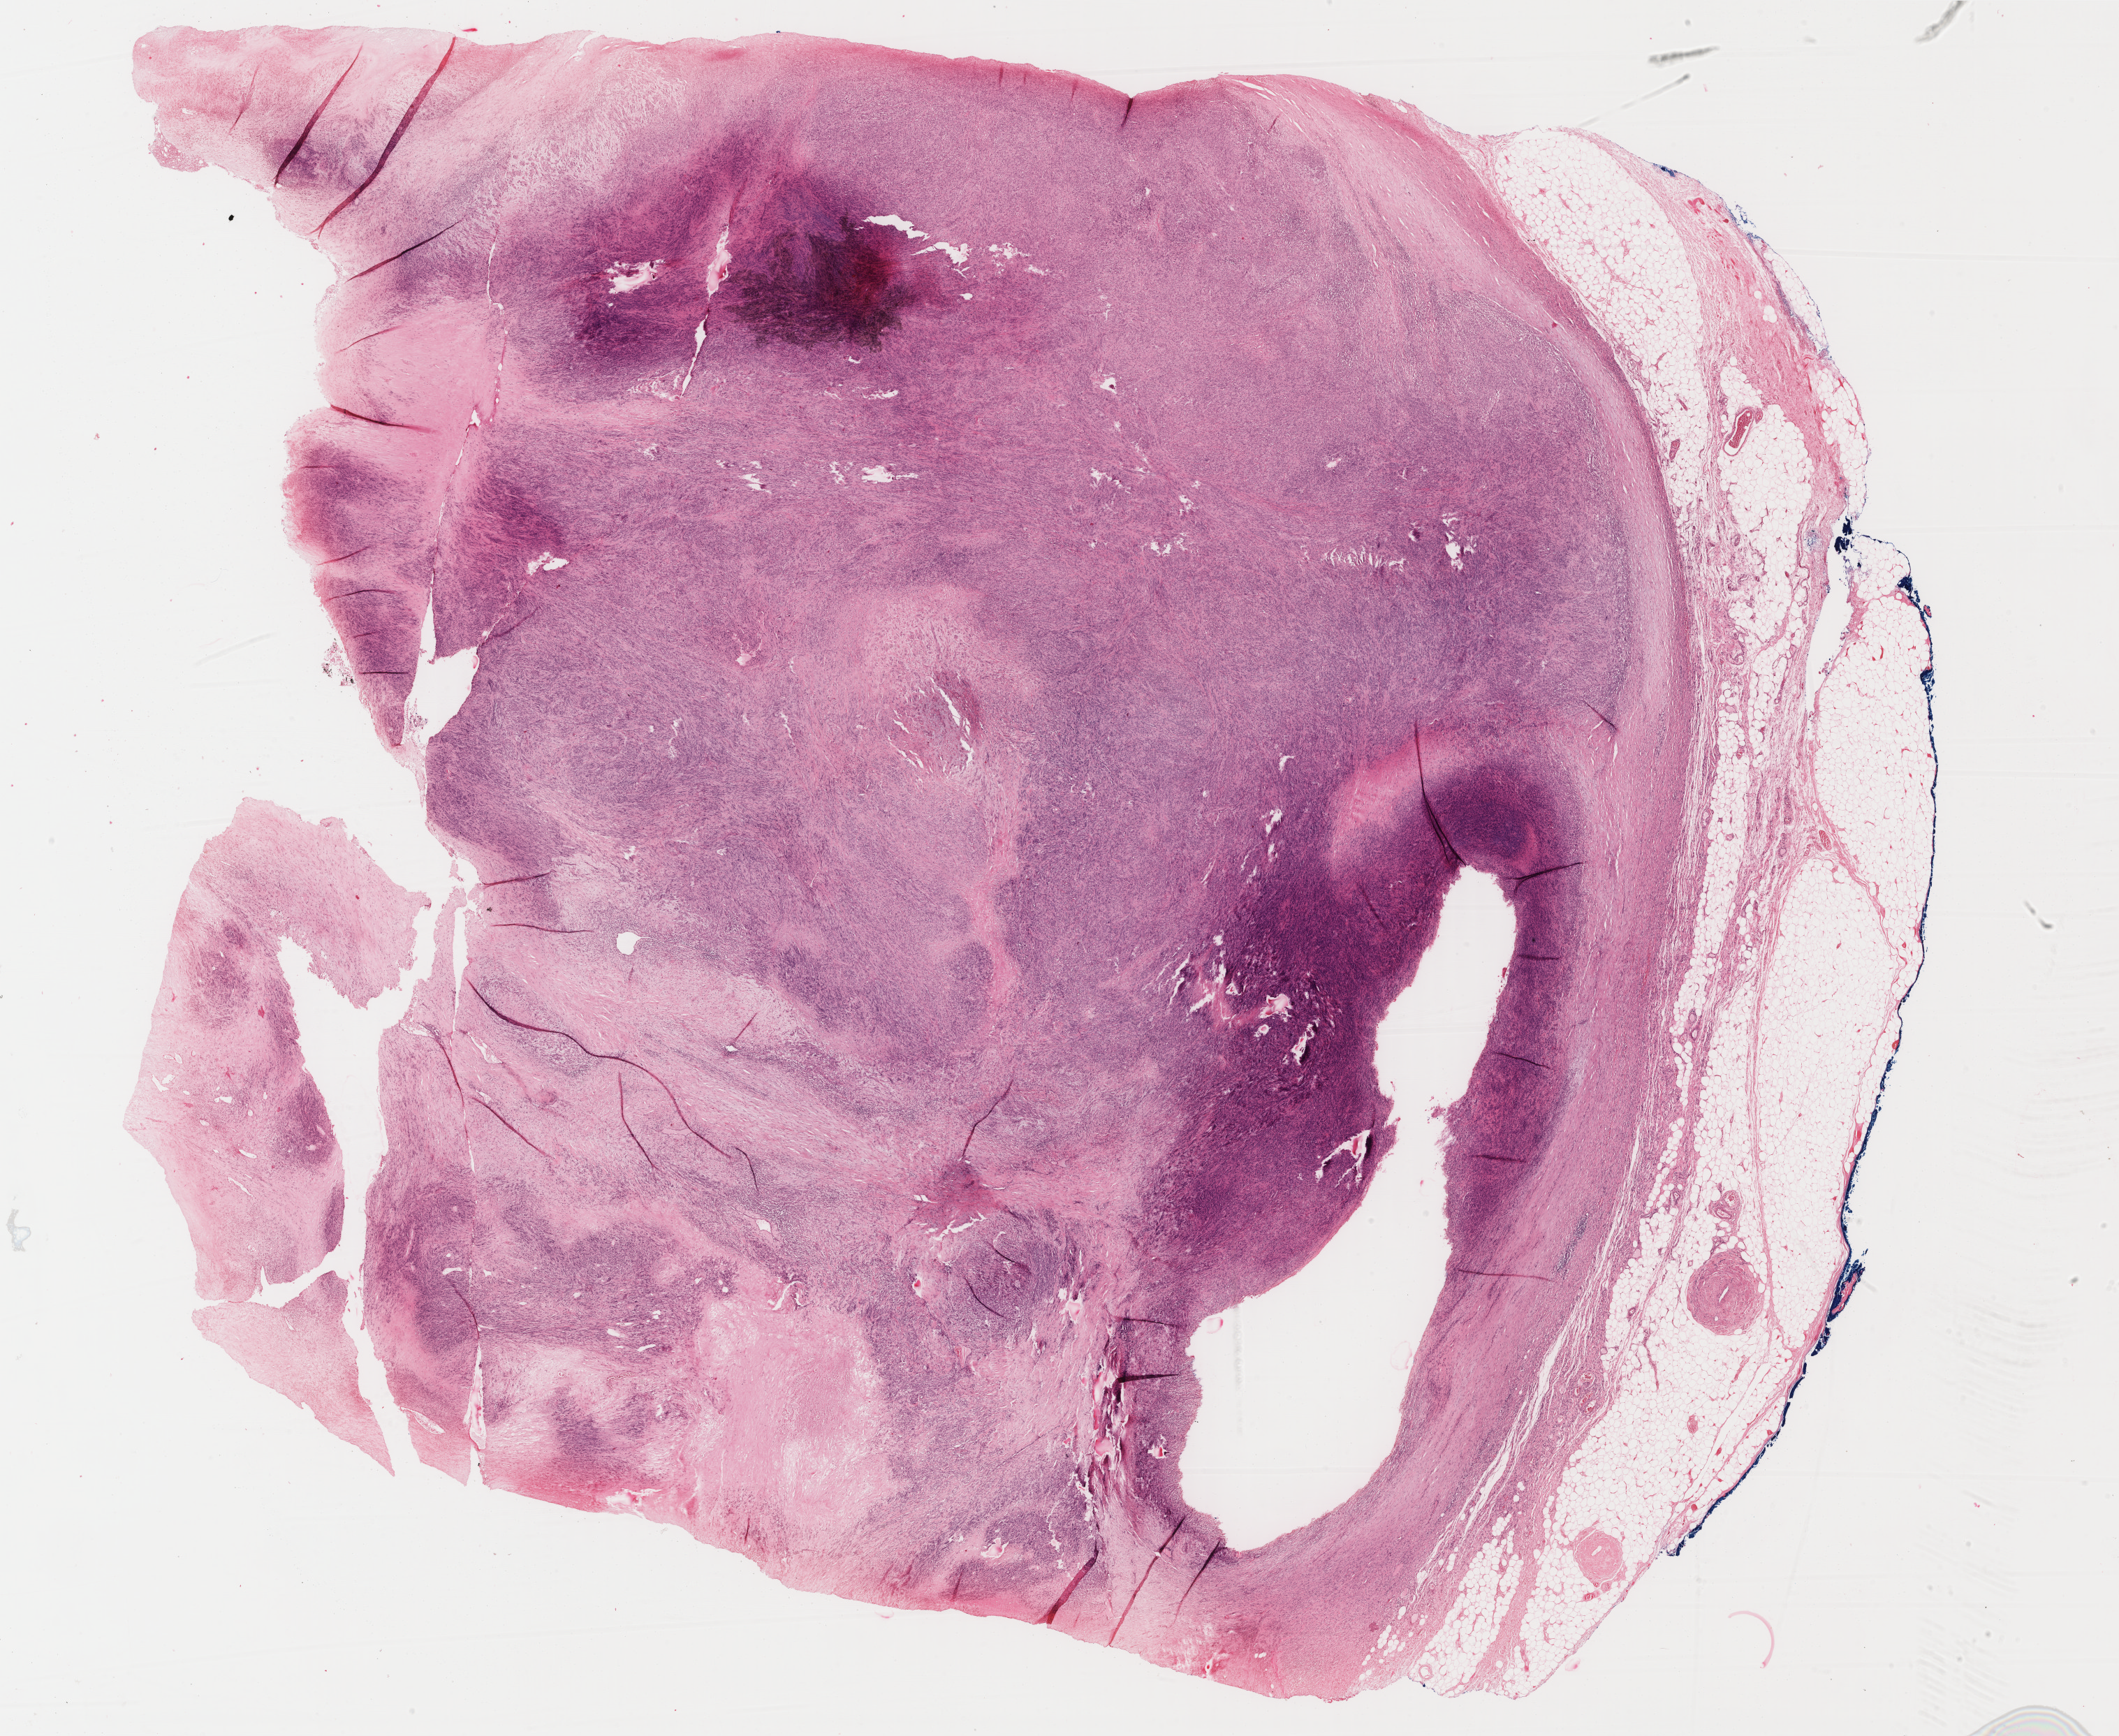
H&E-stained whole-slide image — a low-resolution overview of the entire scanned area, about 24.1 x 19.7 mm. FFPE section. Sample: primary tumour, skin. Male, age 43 years at initial diagnosis.
• diagnosis: Malignant melanoma, NOS